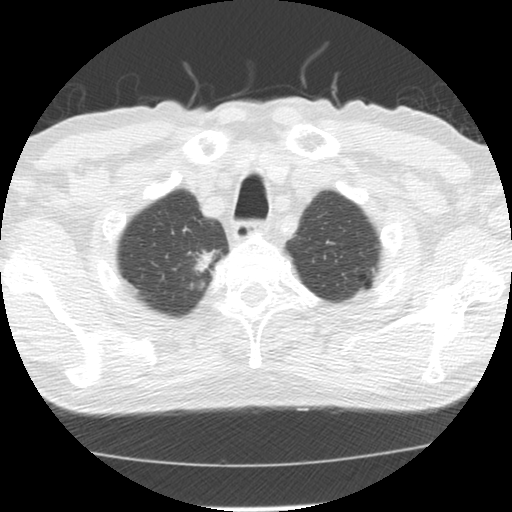
Low-dose screening chest CT, one axial slice; position 119 of 139 along the scan axis; 120 kVp; lung window (W 1500 / L -600 HU); 512 × 512 image matrix, field of view 310 × 310 mm.
Structures marked on this image (manually delineated by an expert):
- lesion 1 (tumor, upper lobe of right lung): bounding box [x1, y1, x2, y2] px = [194, 249, 218, 273]